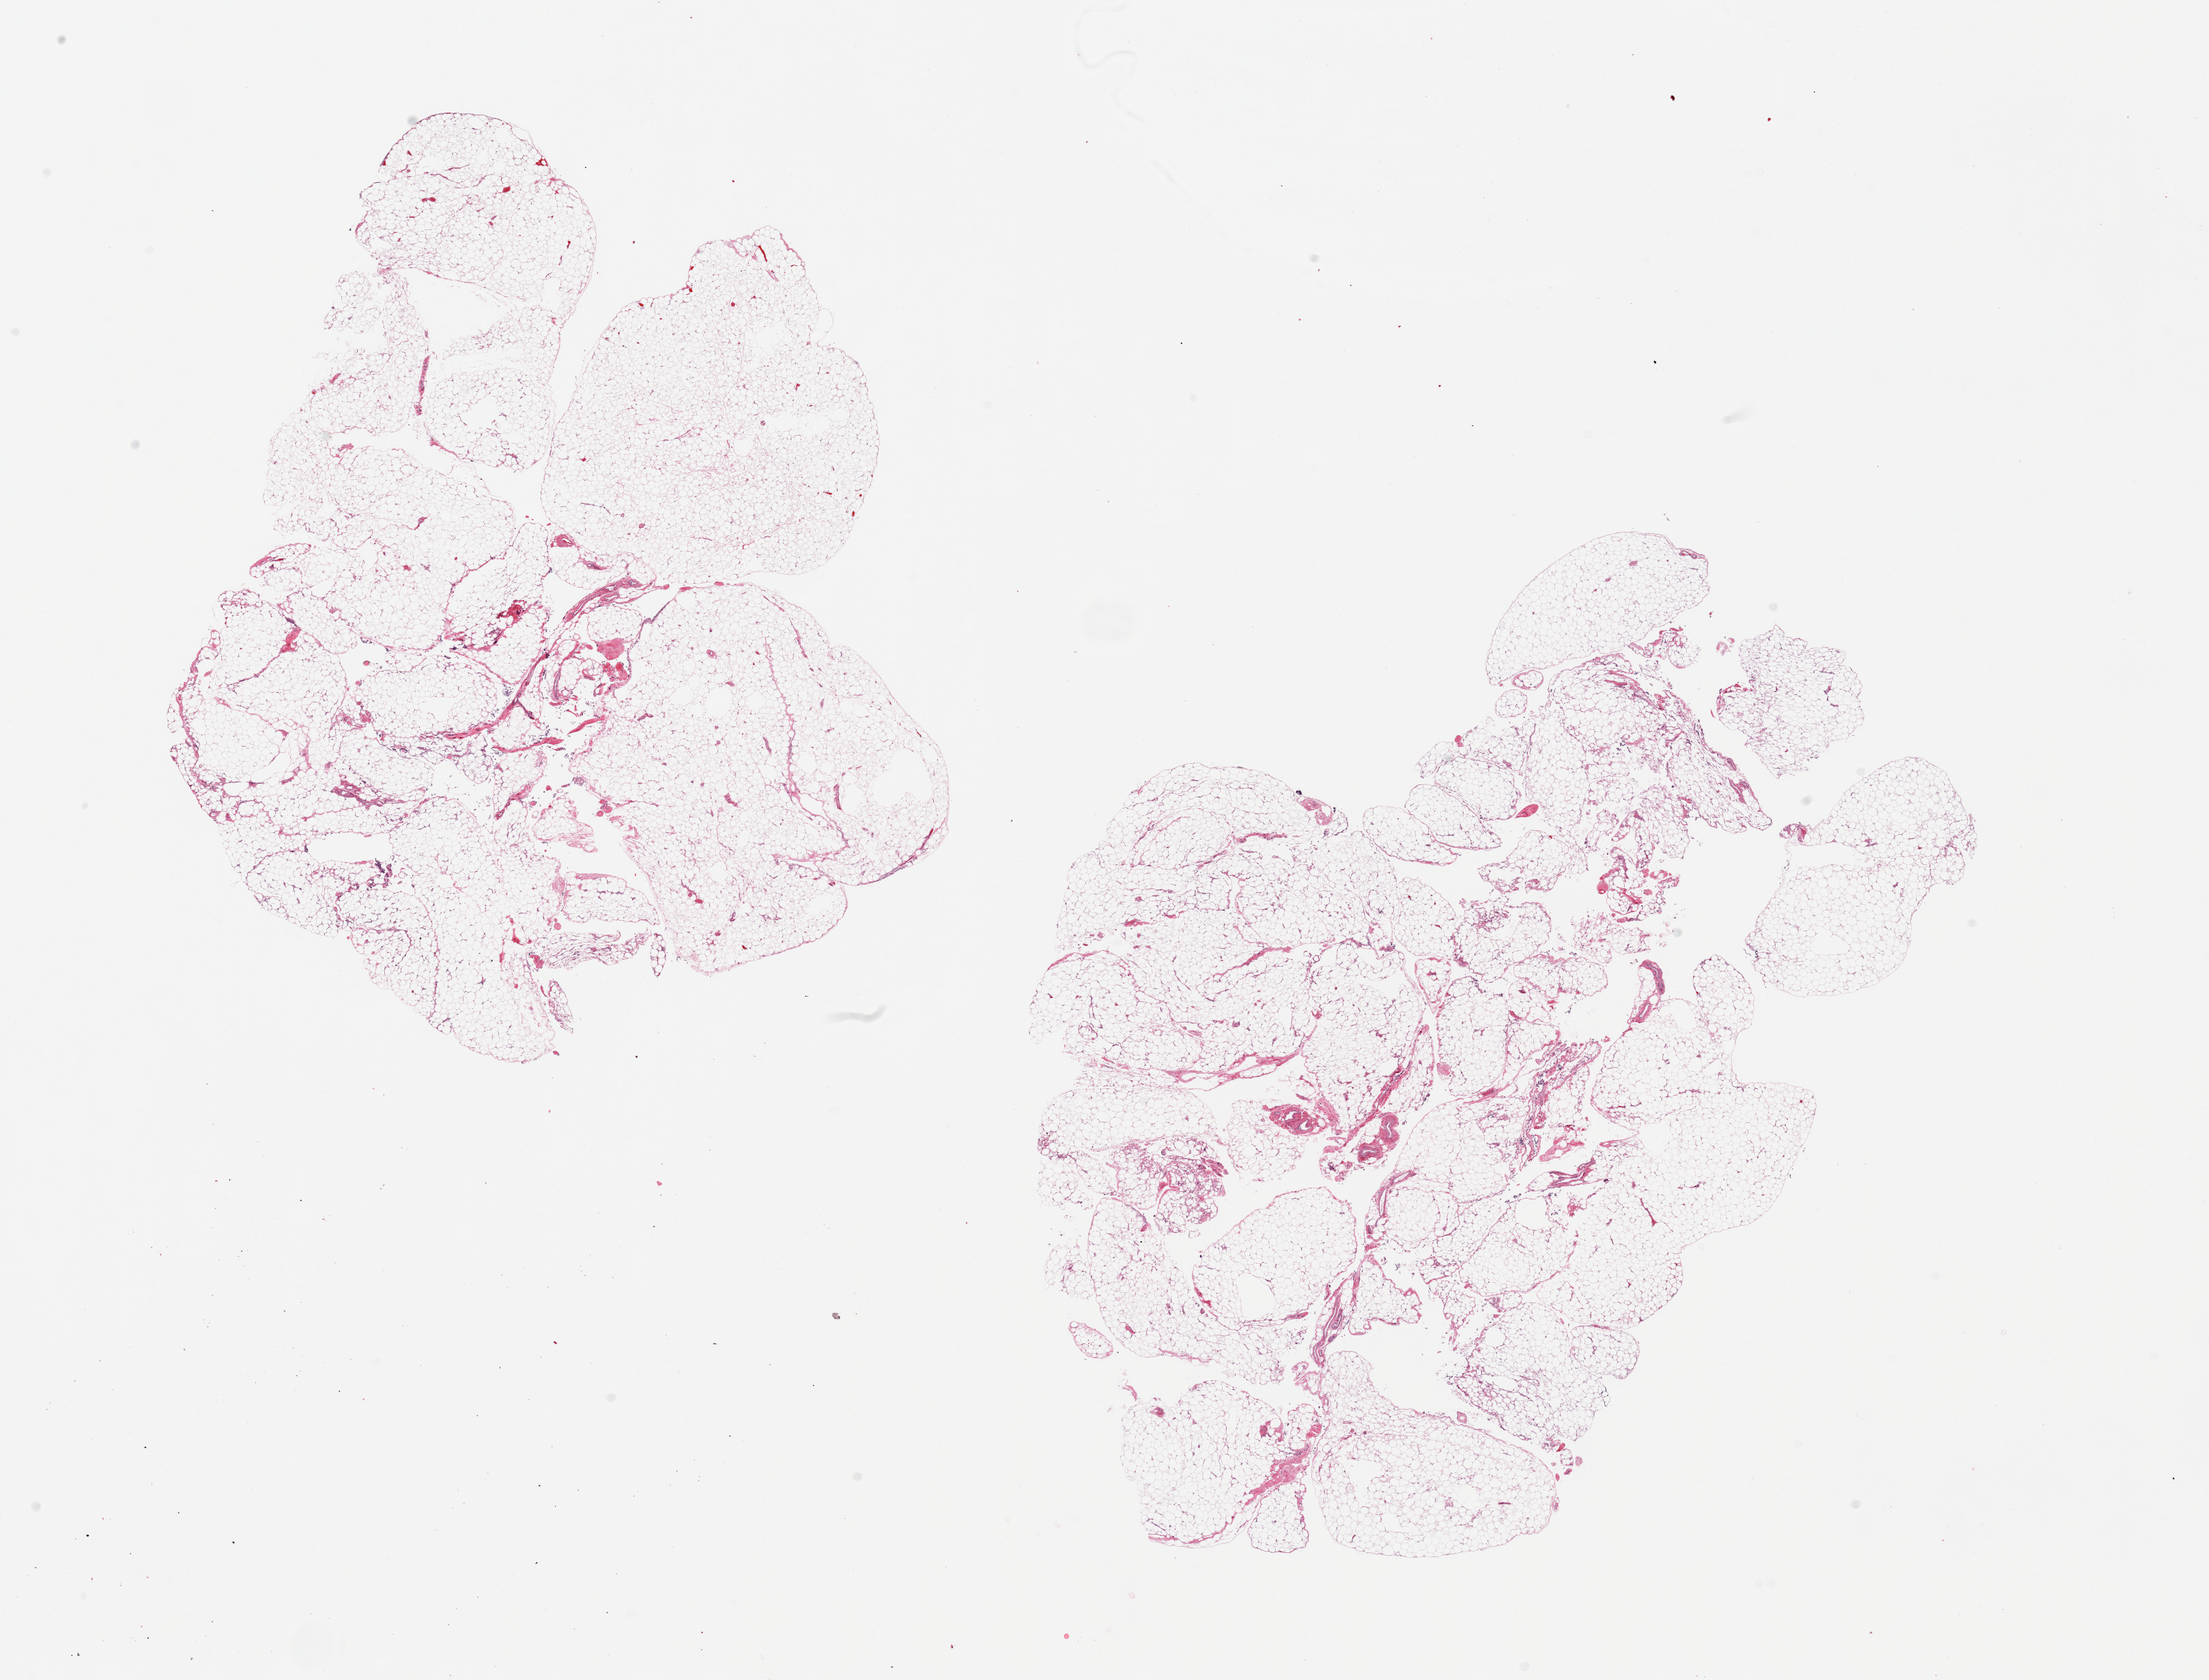
Digitized hematoxylin and eosin (H&E)-stained section, whole scanned area (about 25.6 x 19.5 mm, slide scanned at 20x) shown as a low-resolution overview; PAXgene-fixed paraffin-embedded (PFPE) section; sampled site (target tissue): omentum; tissue donor sample. Female donor.
- reviewer comment on this tissue sample: 2 pieces